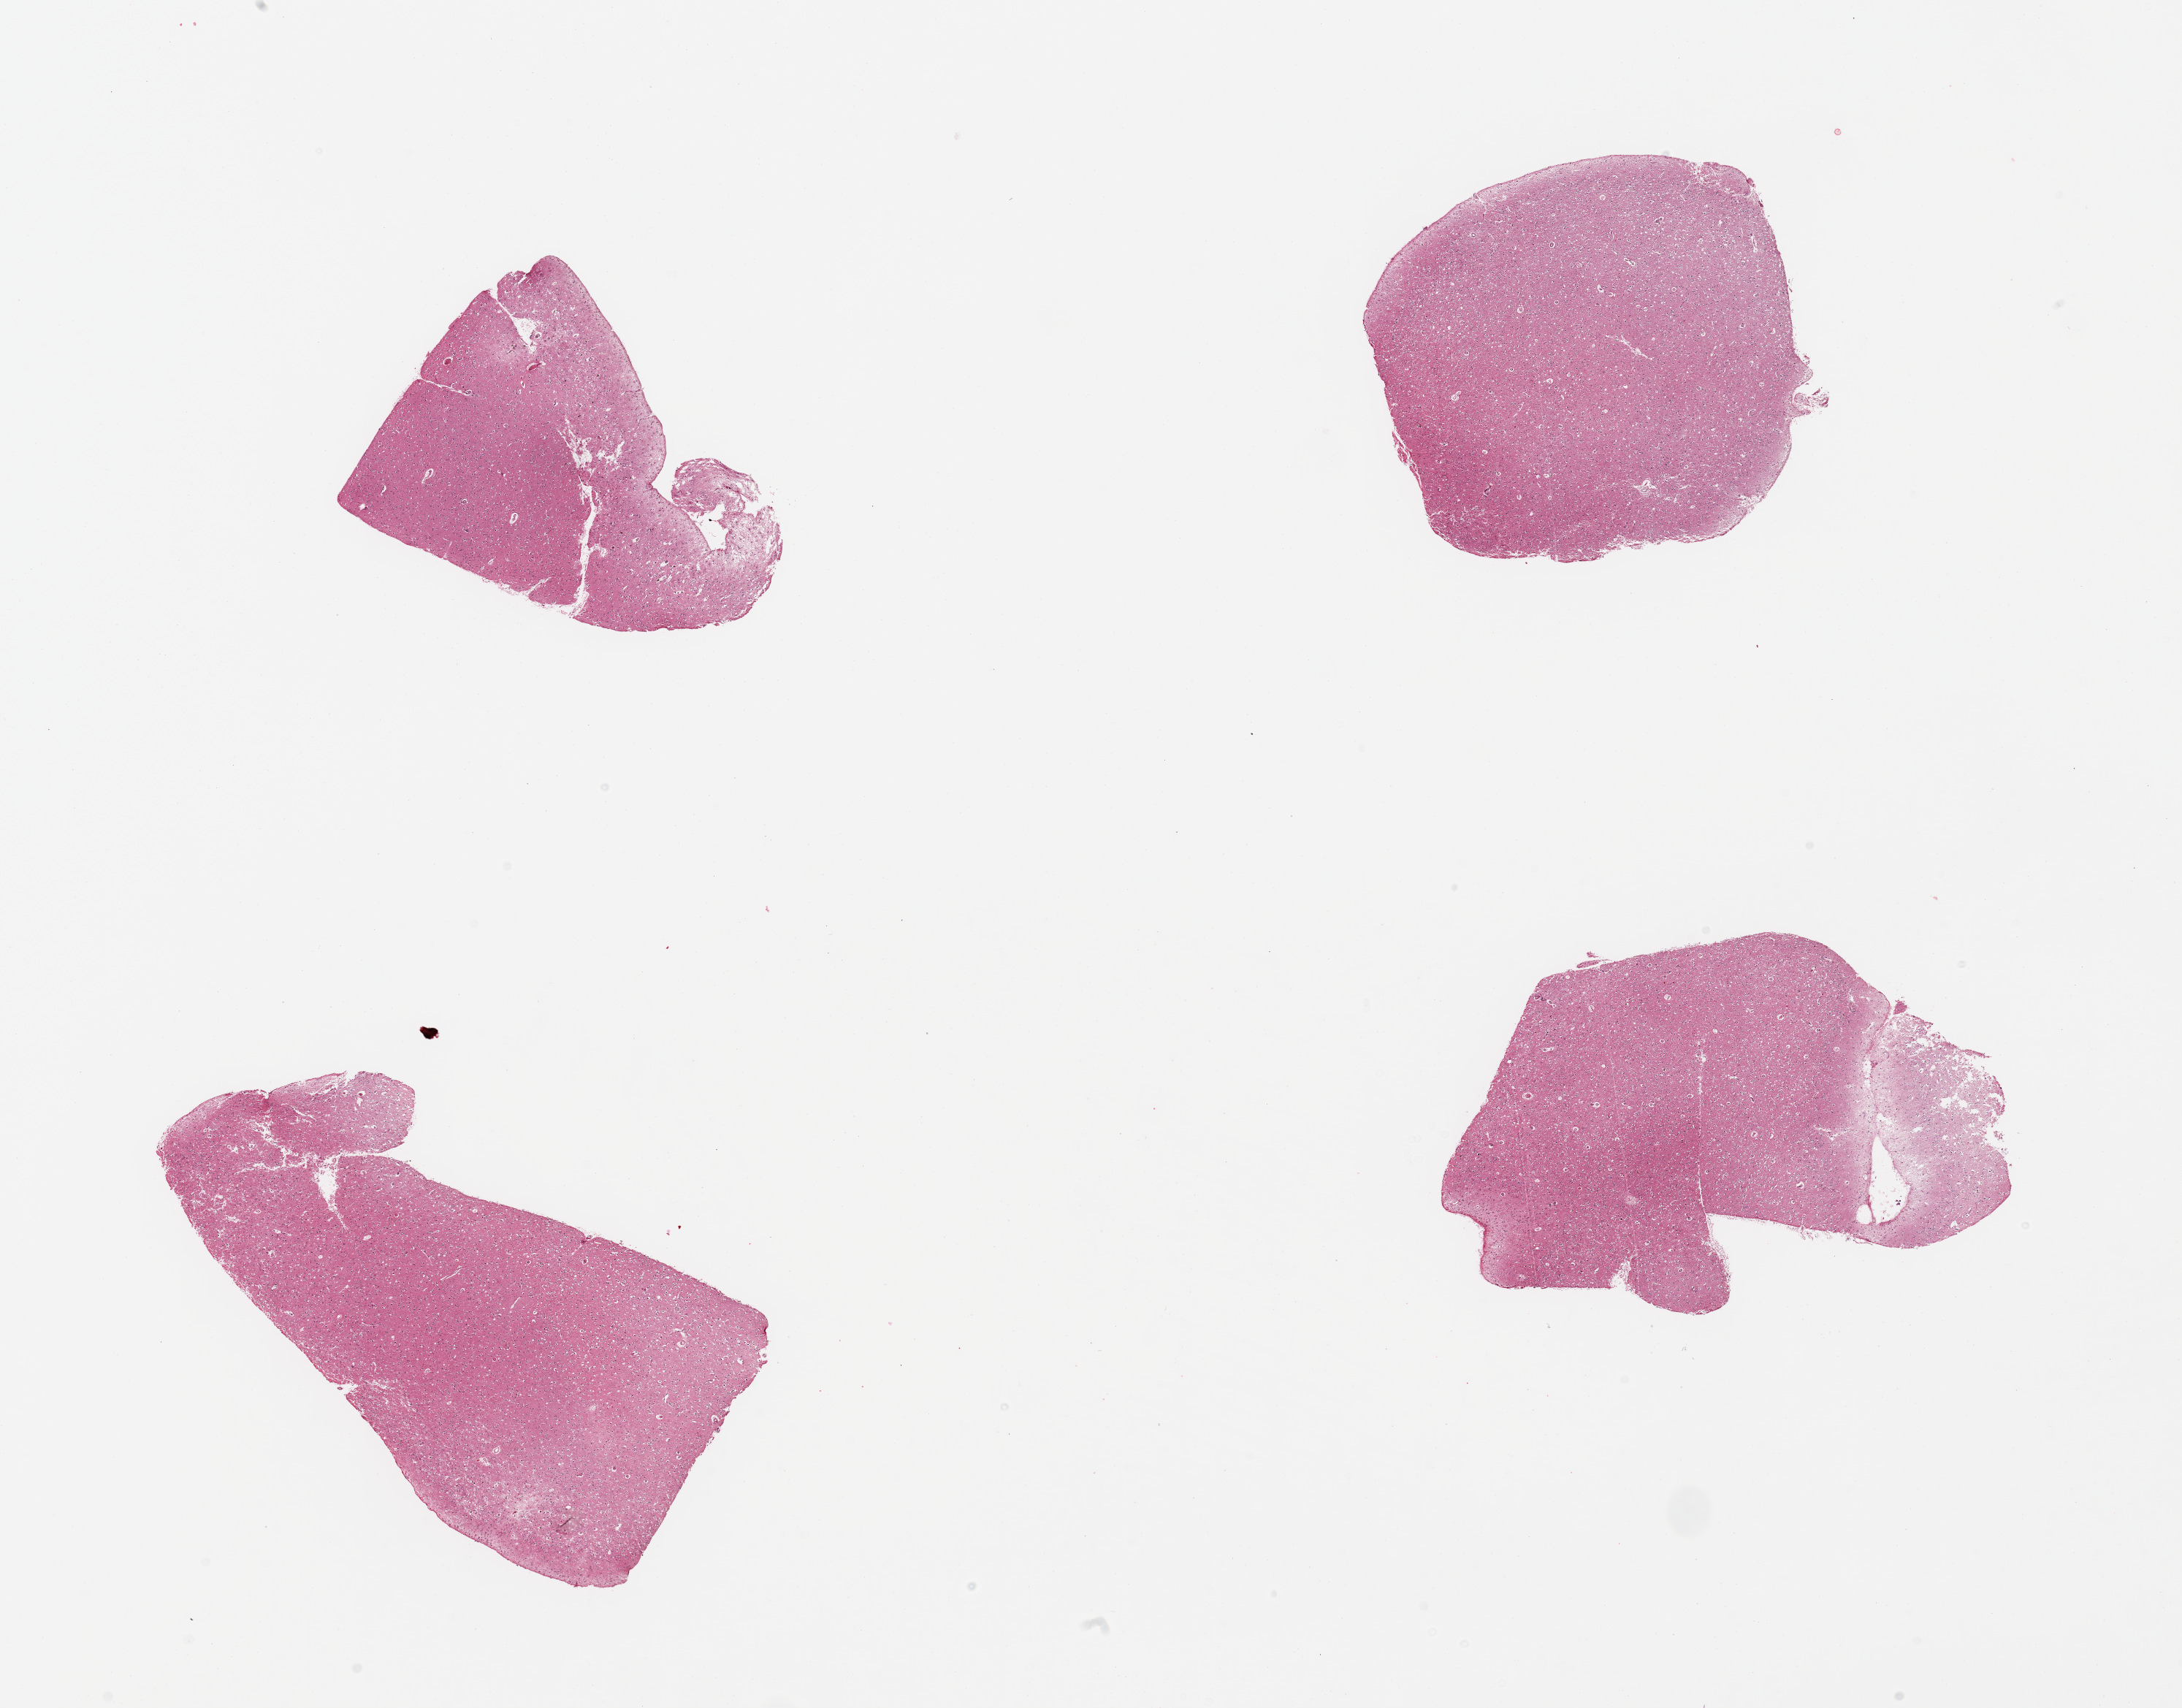
Digitized hematoxylin and eosin (H&E)-stained section — shown as a low-resolution overview of the whole scanned area (about 23.6 x 18.5 mm); PAXgene-fixed, paraffin-embedded tissue; sampled site (target tissue): cerebral cortex; tissue donor sample.
Reviewer comment on this tissue sample: 4 pieces, no abnormalities.